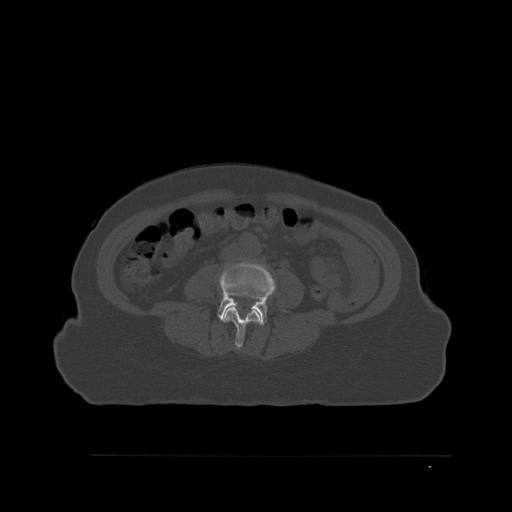
CT including the spine, one axial slice; slice 215 of 527 in the series (ordered by position); bone window (W 1800 / L 400 HU); 1.5 mm slice thickness; 512 × 512 image matrix. Patient: female, 73 years. From the clinical record (not read from this slice): primary cancer: breast.
Structures marked on this image (semi-automatically segmented with operator editing):
- L3 vertebra: box from (x=223, y=305) to (x=262, y=349) px
- L4 vertebra: (x=217, y=262)–(x=276, y=325)